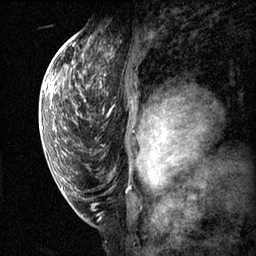
Breast MRI (dynamic contrast-enhanced), one sagittal slice; position 40 of 60 along the scan axis; dynamic contrast-enhanced series, image 2 of 3 at this slice position (ordered by acquisition); 1.5 T; TE 4.2 ms, TR 11.1 ms; 256 × 256 image matrix, field of view 180 × 180 mm. Female patient, age 50 years.
Outlined on this slice (semi-automatically segmented with operator editing):
- analysis volume of interest (the breast-tissue region the enhancement analysis was run in; not a lesion): bounding box <82,56,166,143> (left, top, right, bottom; pixels)
- tumour enhancement mask (voxels above the 70 % enhancement threshold inside the analysis volume of interest): <141,116,164,143>